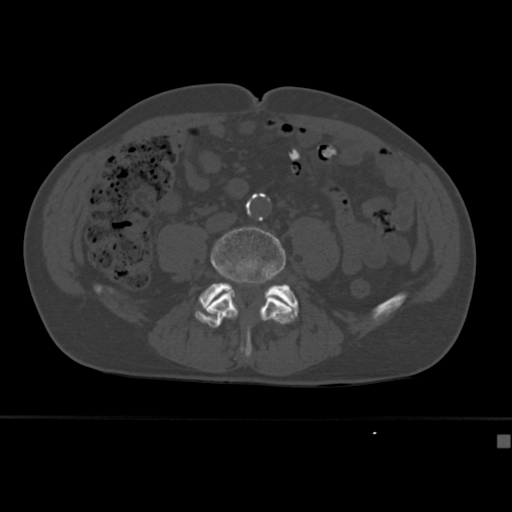
CT including the spine, one axial slice. Slice 99 of 430 in the series (ordered by position). Reconstruction kernel Br40s. Bone window (W 1800 / L 400 HU). 512 × 512 image matrix, field of view 337 × 337 mm. Patient: male, 64 years. Case-level facts recorded for this patient, not image findings: primary cancer: uterus; vertebrae with lytic lesions (as recorded): T1, T4, T5, T7, L5.
Outlined on this slice (semi-automatically segmented with operator editing):
- L4 vertebra: bounding box <204,226,292,355> (left, top, right, bottom; pixels)
- L5 vertebra: <199,282,299,356>